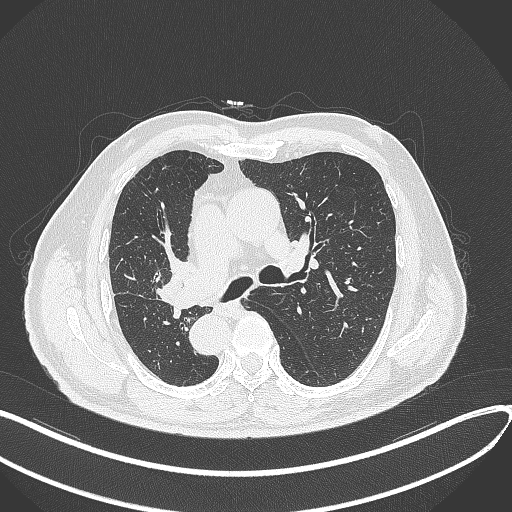
Chest CT, one axial slice. Slice 182 of 300 in the series (ordered by position). 120 kVp. Lung window (W 1500 / L -600 HU). 1 mm slice thickness. 512 × 512 image matrix. Male patient, age 67 years. From the clinical record (not read from this slice): clinical TNM (as recorded): T2a N0 M0.
Structures marked on this image (rectangle marked by the reading radiologist):
- lung tumour (recorded histology: squamous cell carcinoma): bounding box [x1, y1, x2, y2] px = [154, 258, 200, 311]